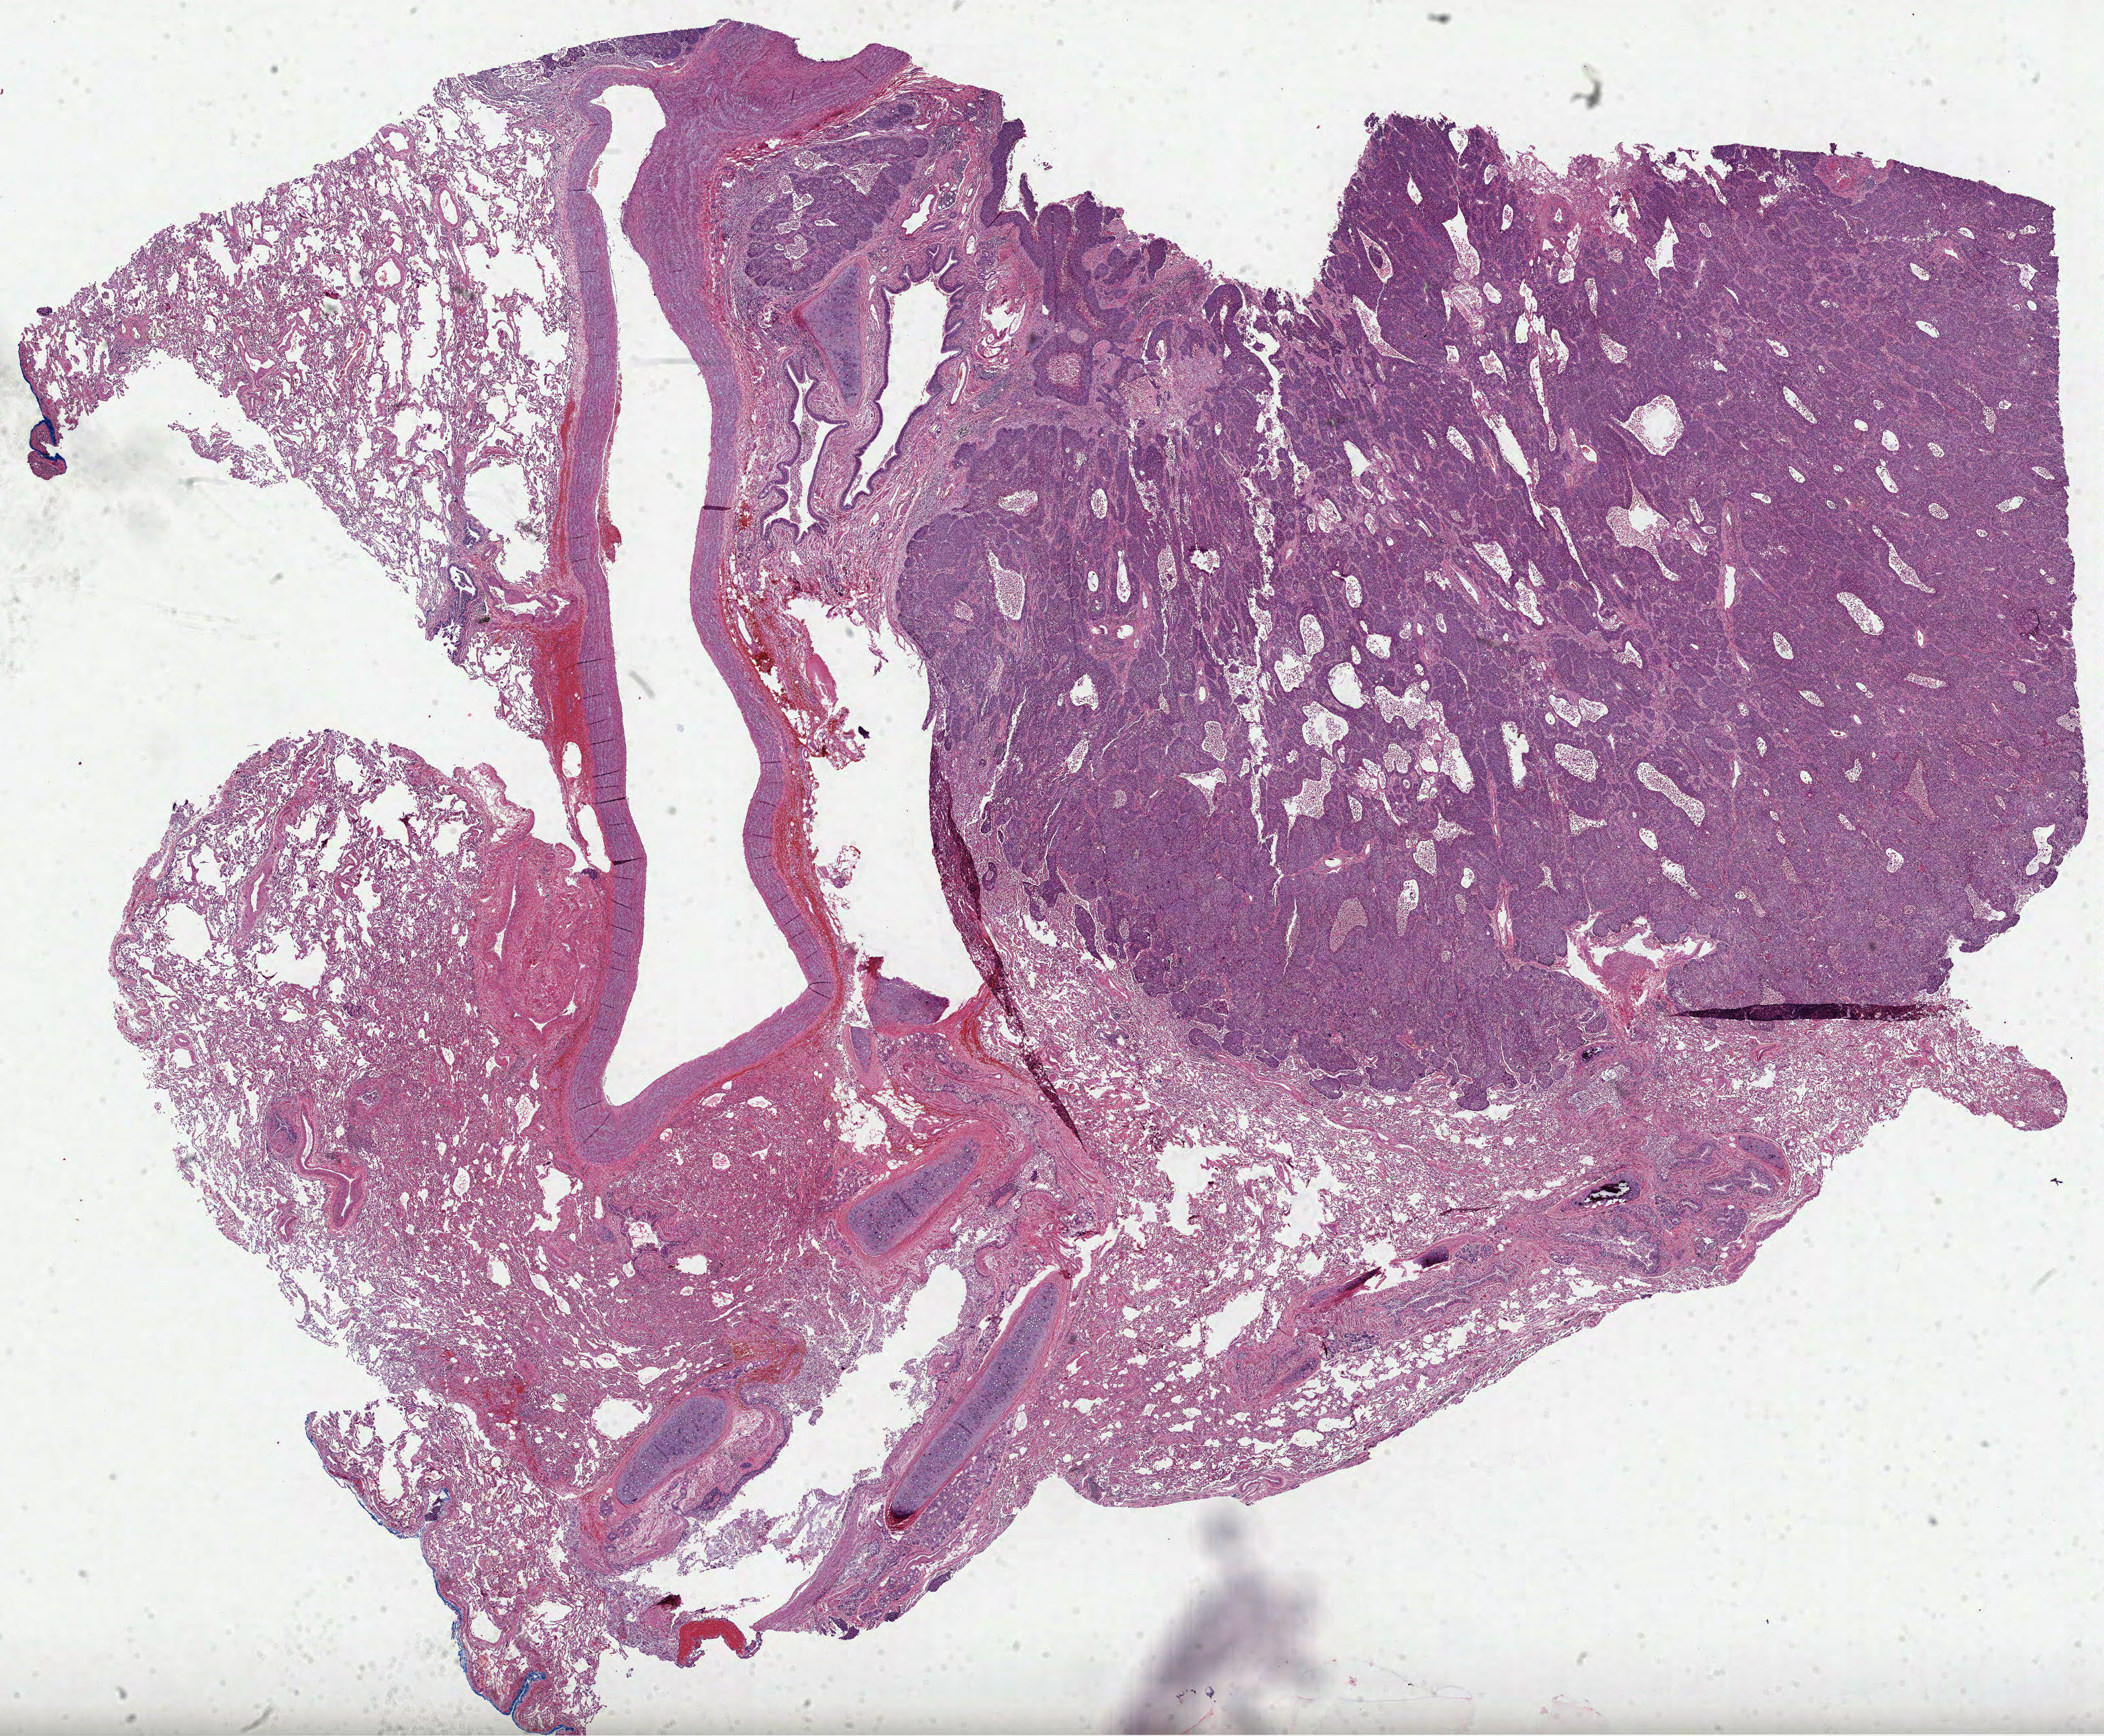
Digitized Hematoxylin and eosin (H&E) stained tissue section (whole slide) — low-resolution overview of the scanned area, about 25.6 x 21.1 mm (from a 40x scan); FFPE section; sample: primary tumour, lung. Patient: female, age at initial diagnosis 73 years.
Histologic diagnosis: Basaloid squamous cell carcinoma. AJCC pathologic stage: IIB (6th edition).